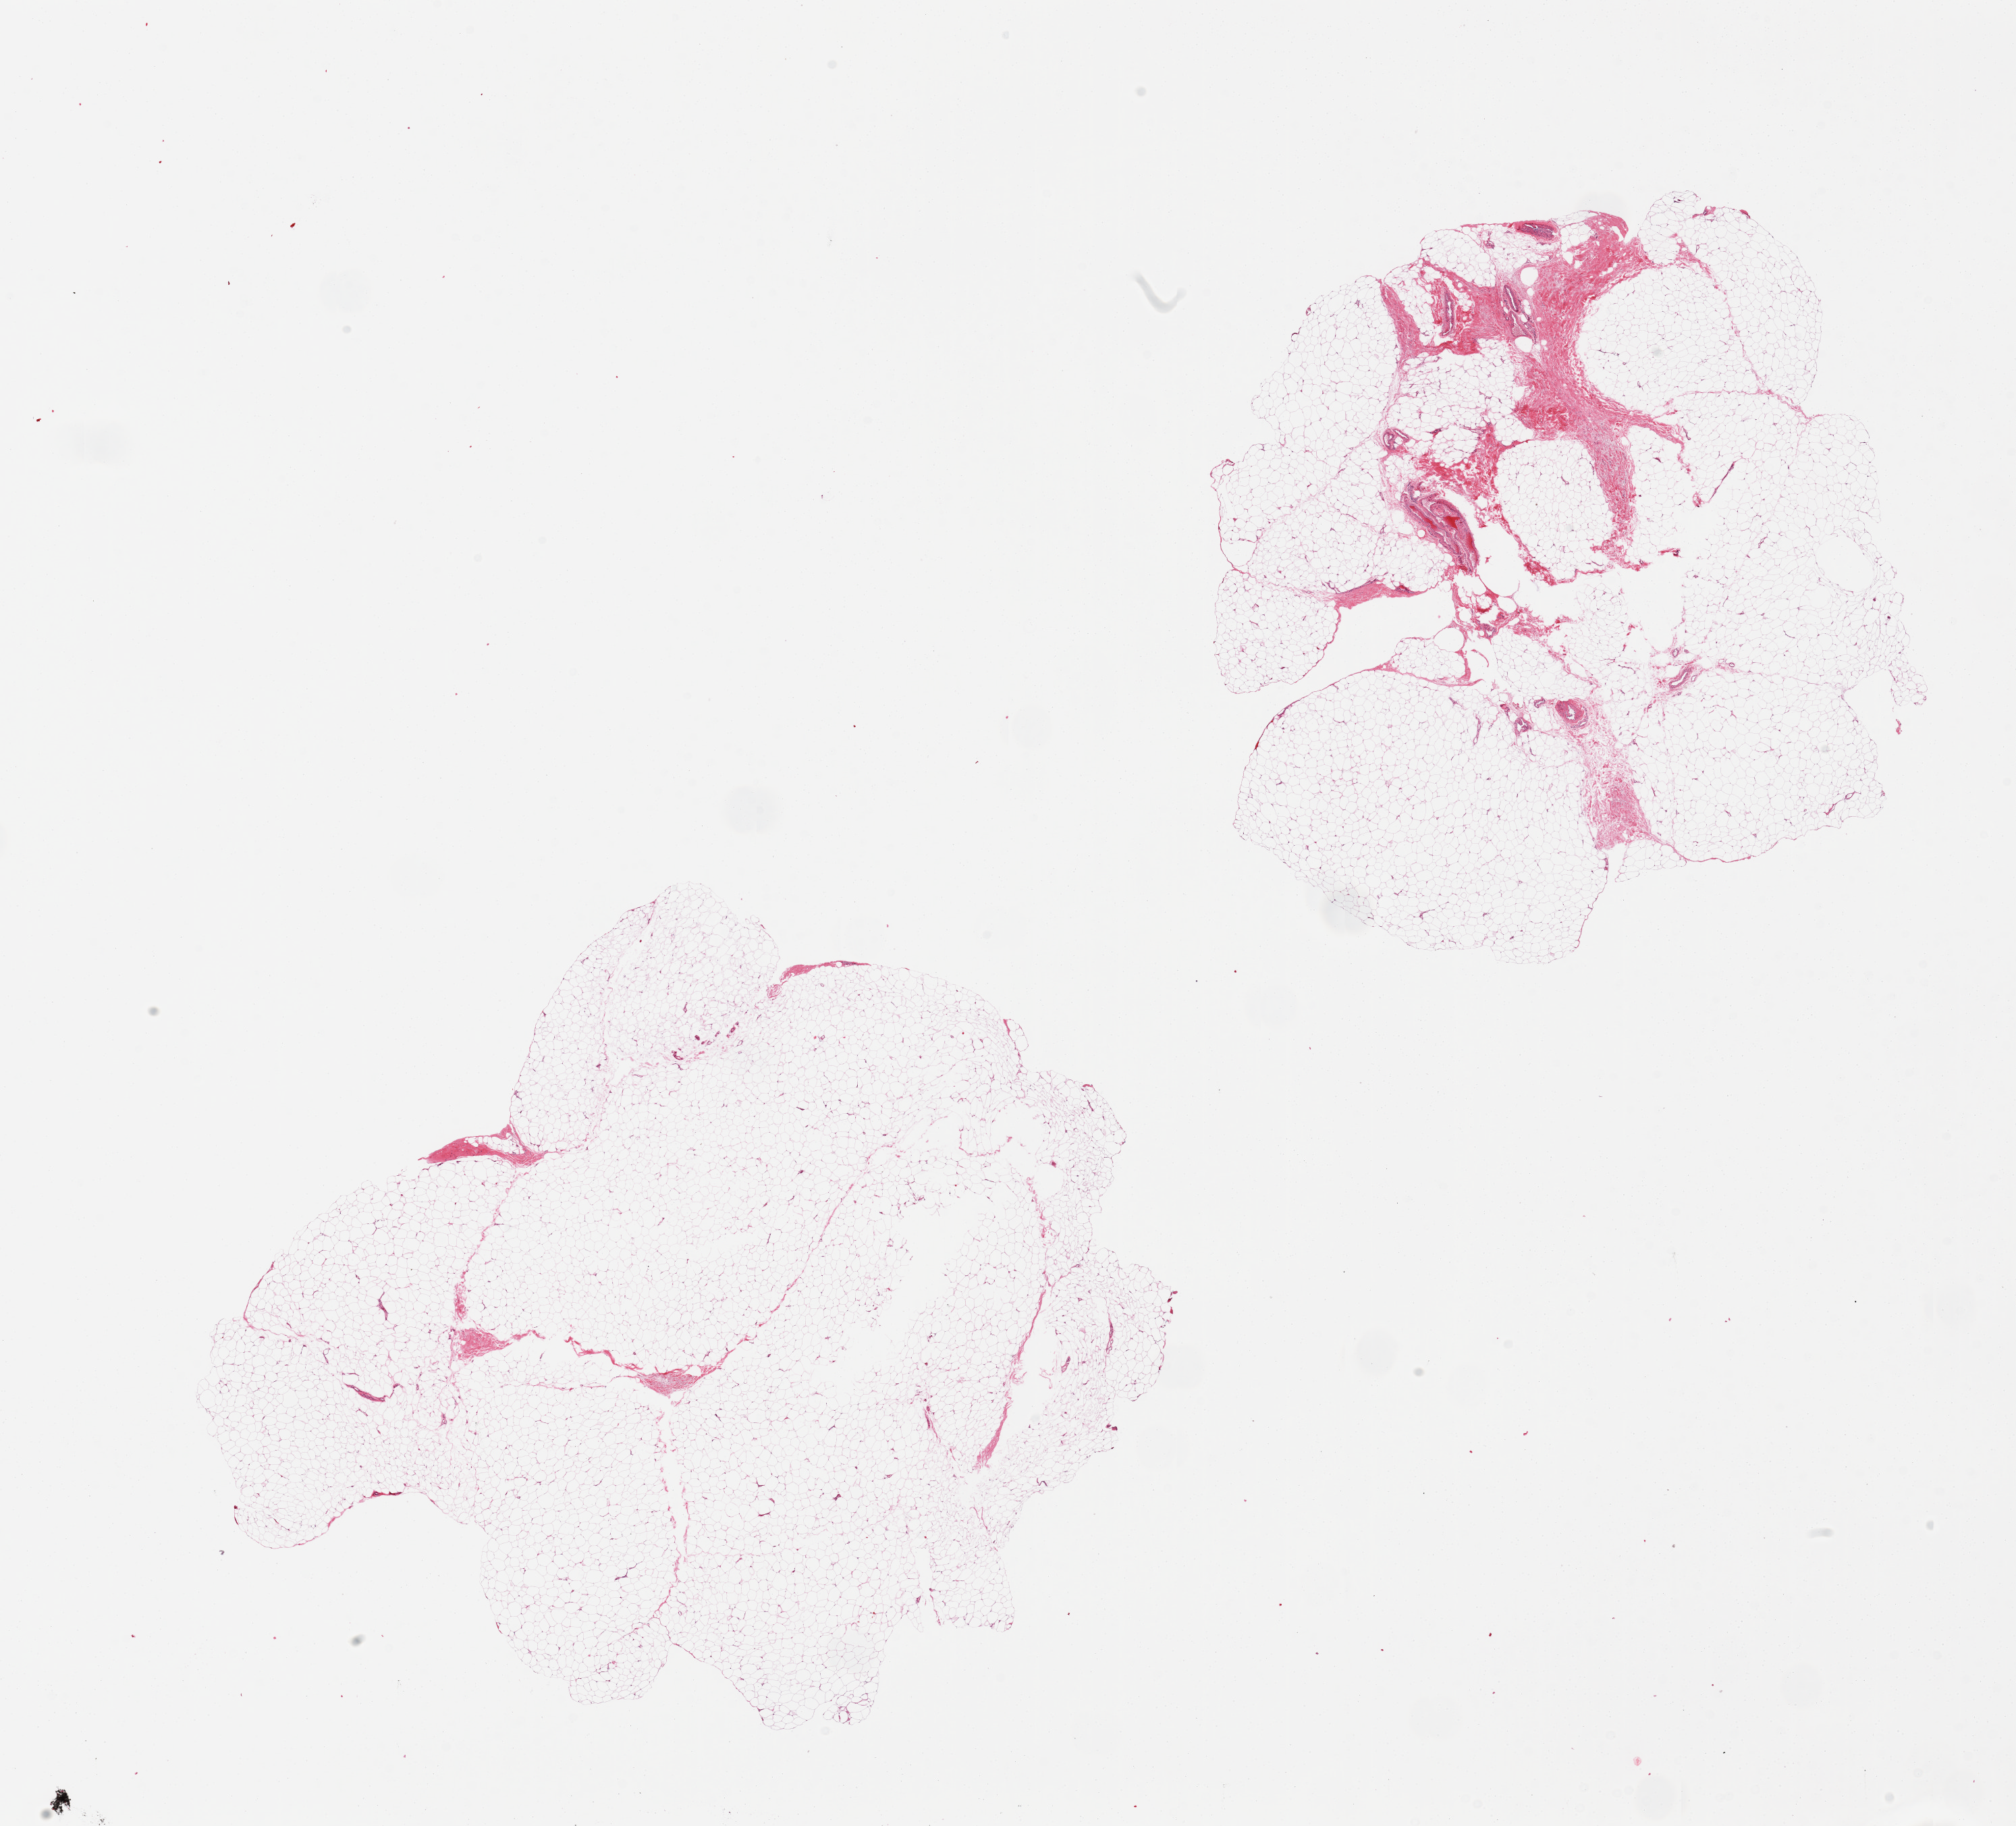
Digitized hematoxylin and eosin (H&E)-stained section, brightfield — shown as a low-resolution overview of the whole scanned area (about 23.6 x 21.4 mm, acquisition: 20x scan). PAXgene-fixed, paraffin-embedded tissue. Sampled site (target tissue): adipose tissue. Donor tissue sample. Male donor.
Review note (as recorded): 2 pieces, ~10-15% fascia/fibrous tissue.